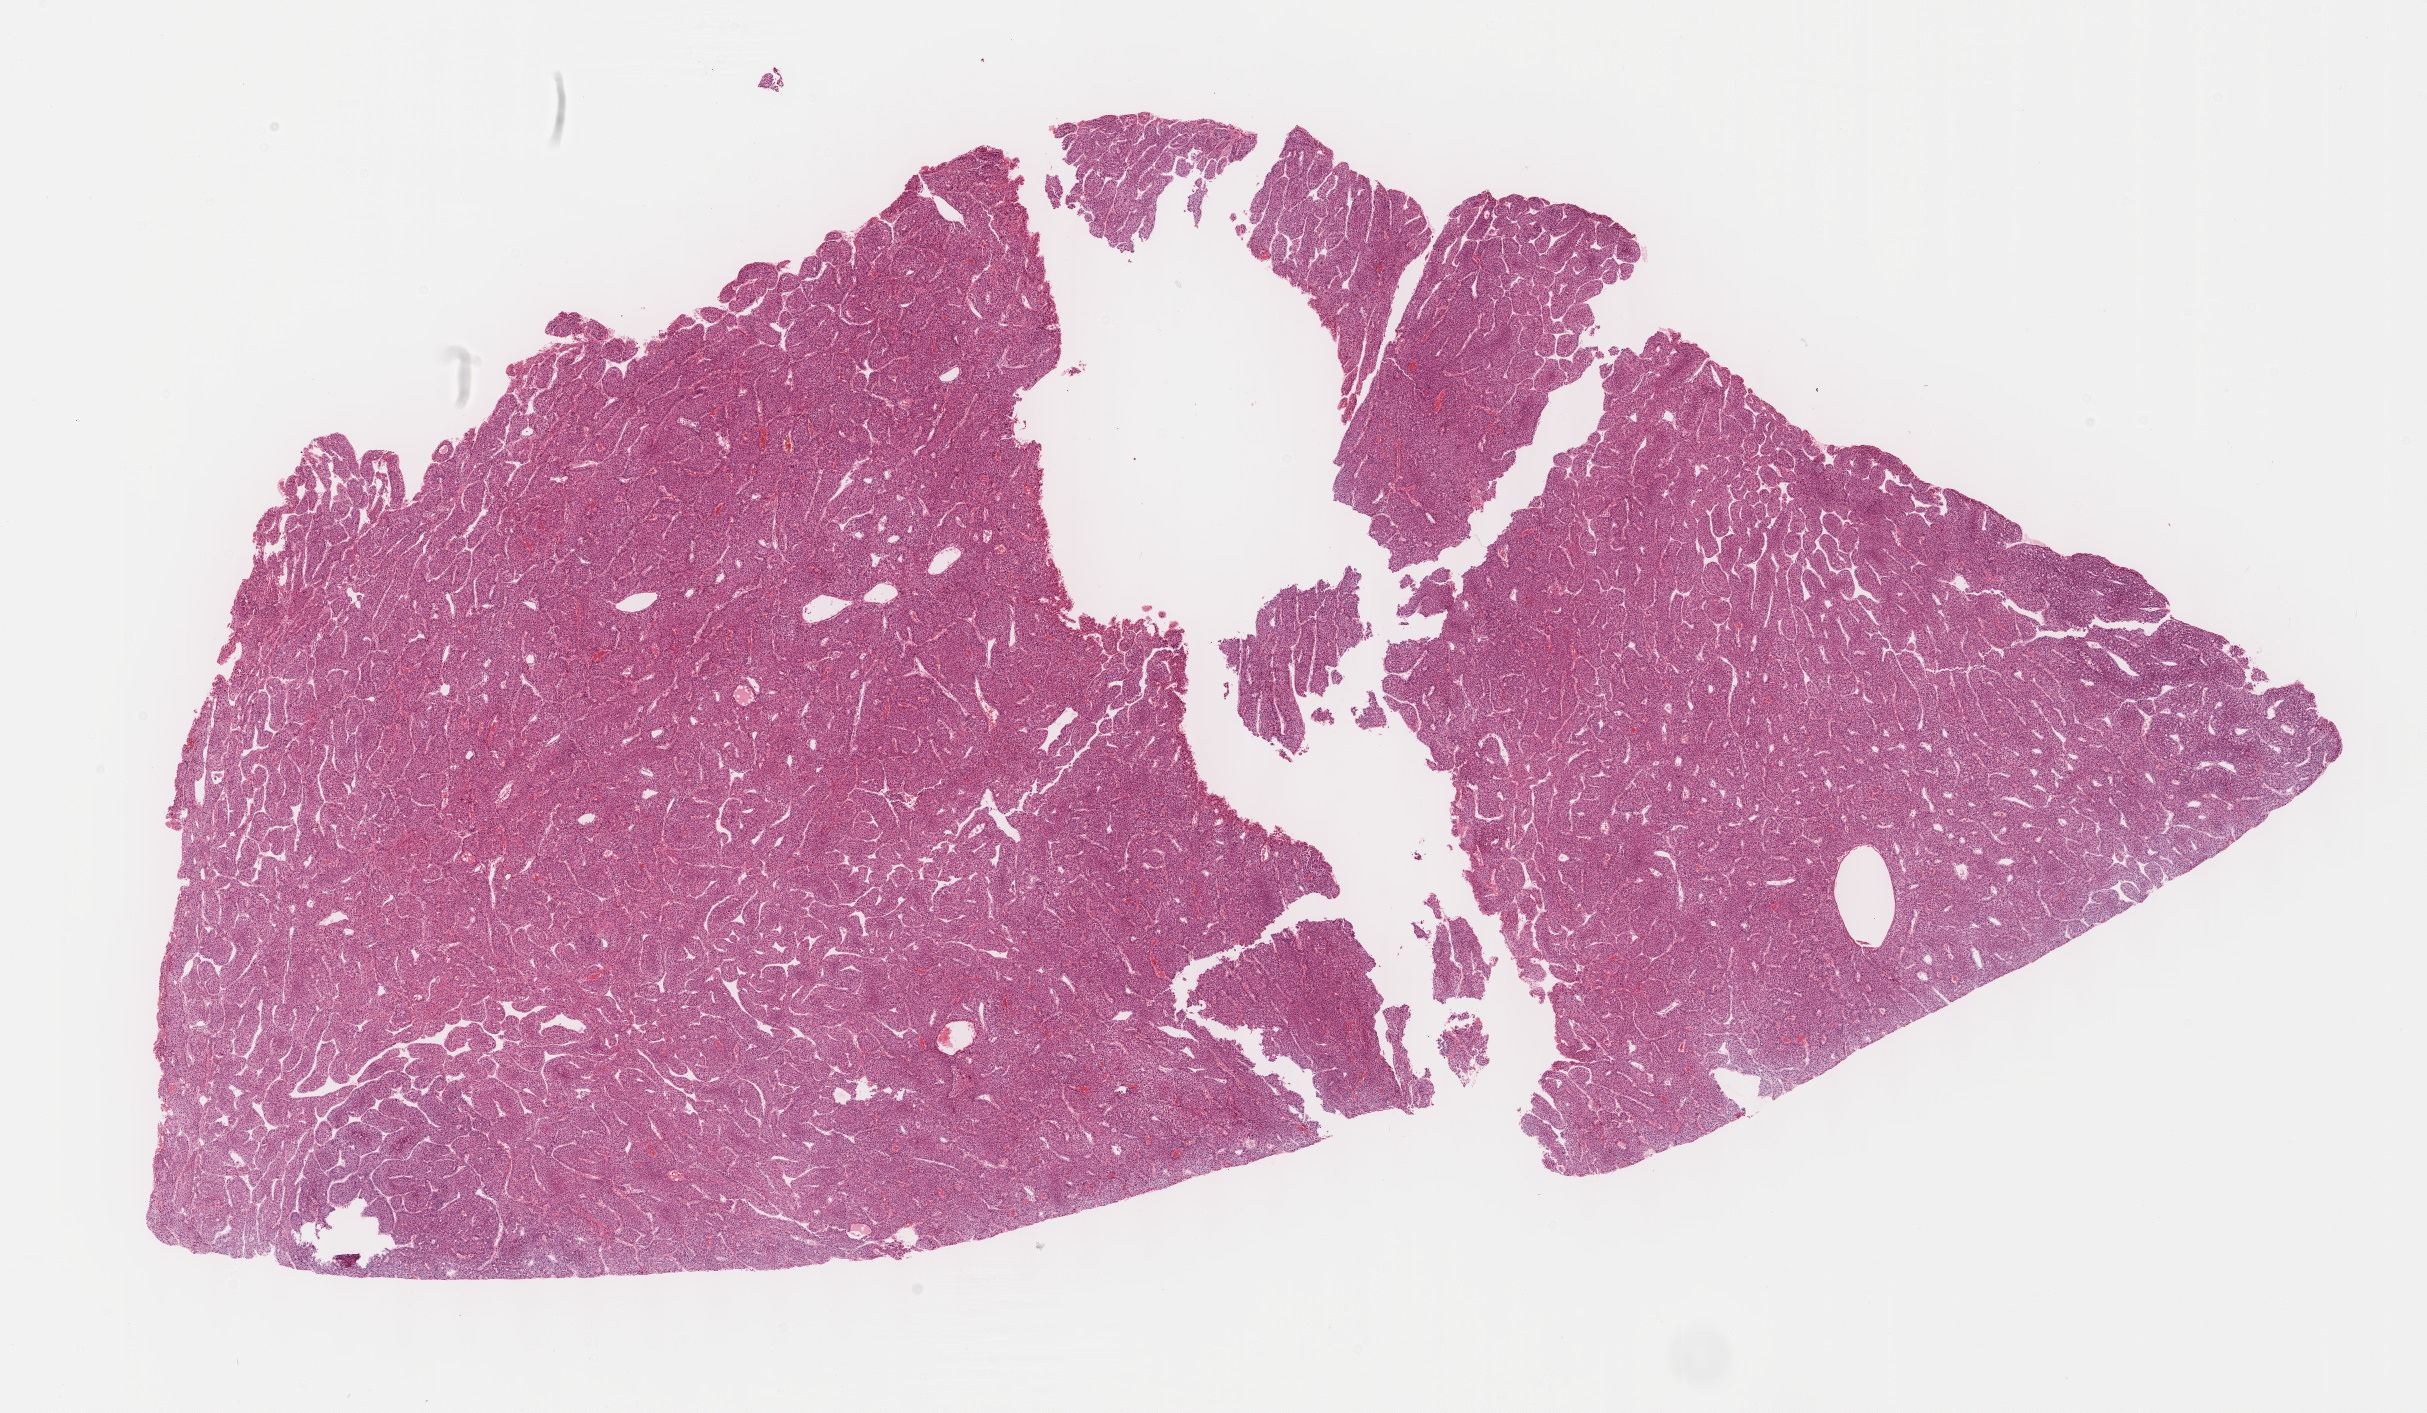
Whole-slide histology image, Hematoxylin and eosin (H&E) stained, a low-resolution overview of the entire scanned area, about 19.6 x 11.4 mm; FFPE section; sample: primary tumour, liver. Patient: male, age at initial diagnosis 51 years. Histologic grade: G3 (poorly differentiated).
- AJCC pathologic stage: I
- diagnosis: Hepatocellular carcinoma, NOS